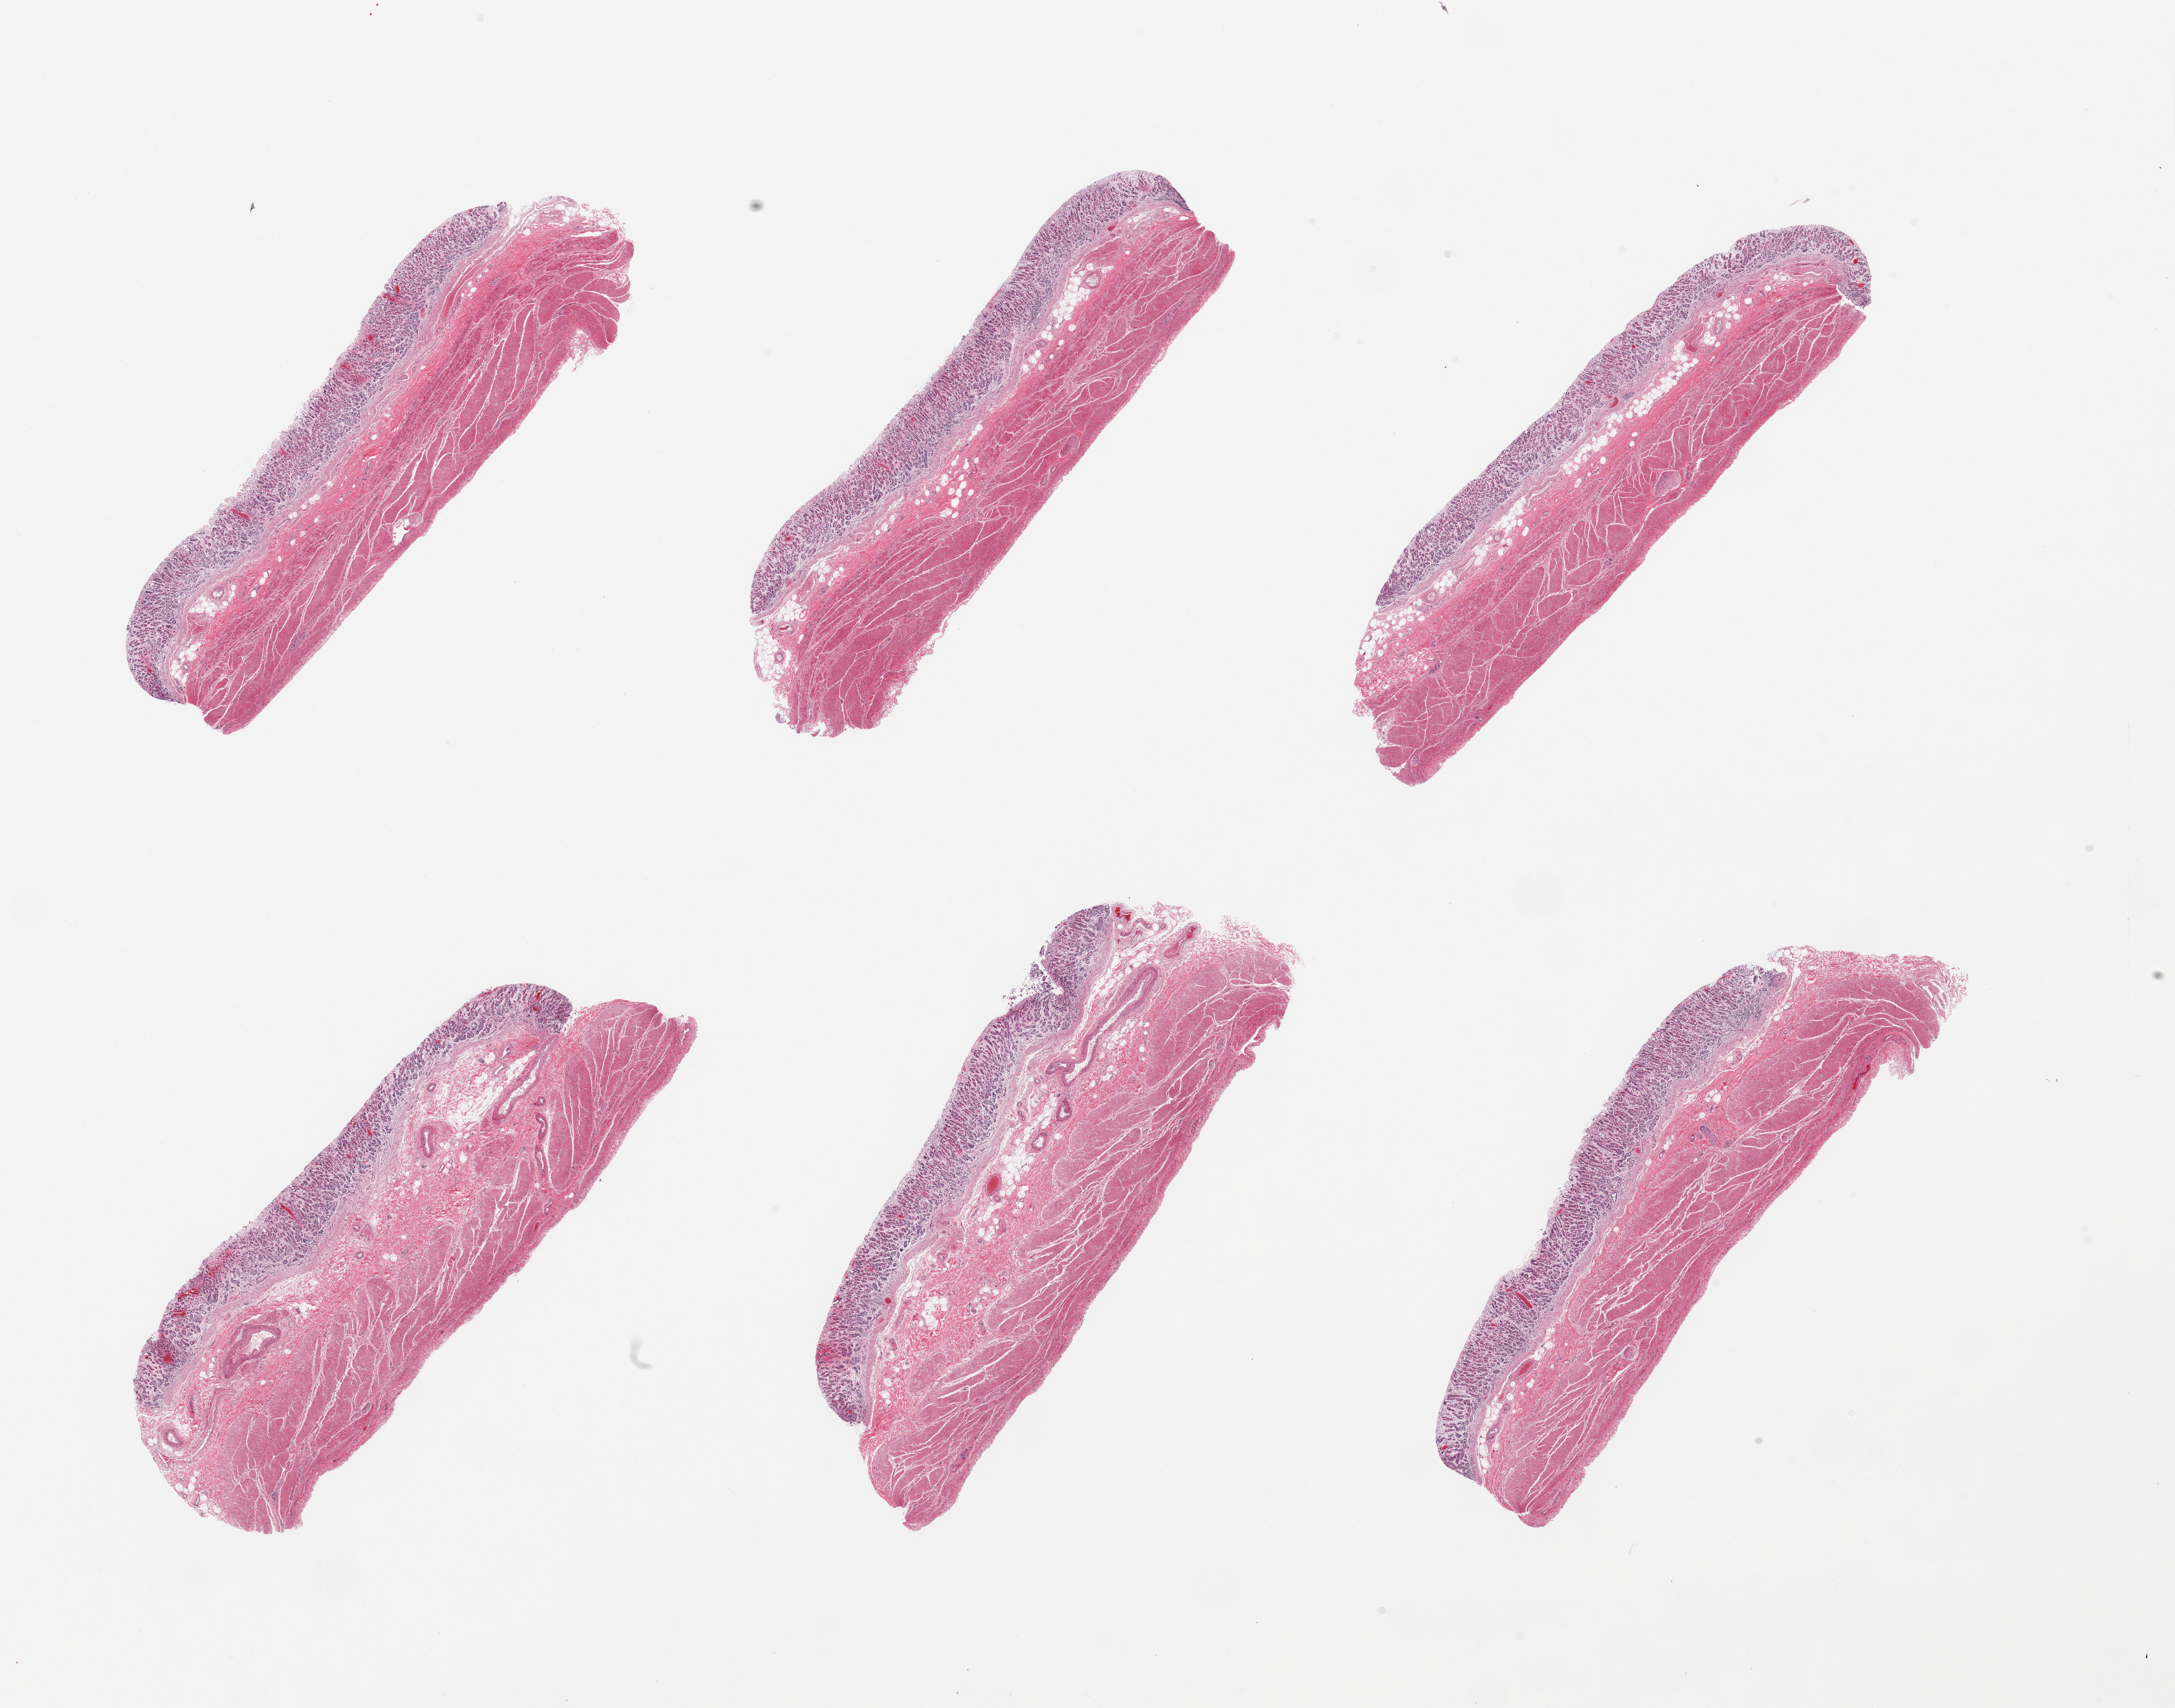
Haematoxylin and eosin whole-slide image, low-resolution overview of the scanned area, about 26.6 x 20.9 mm; PAXgene-fixed, paraffin-embedded tissue; target tissue: stomach; donor tissue sample. Donor: male.
• reviewer comment on this tissue sample: 6 pieces, mucosa up to ~0.5mm, ~20-25% thickness, but with moderate-advanced autolysis